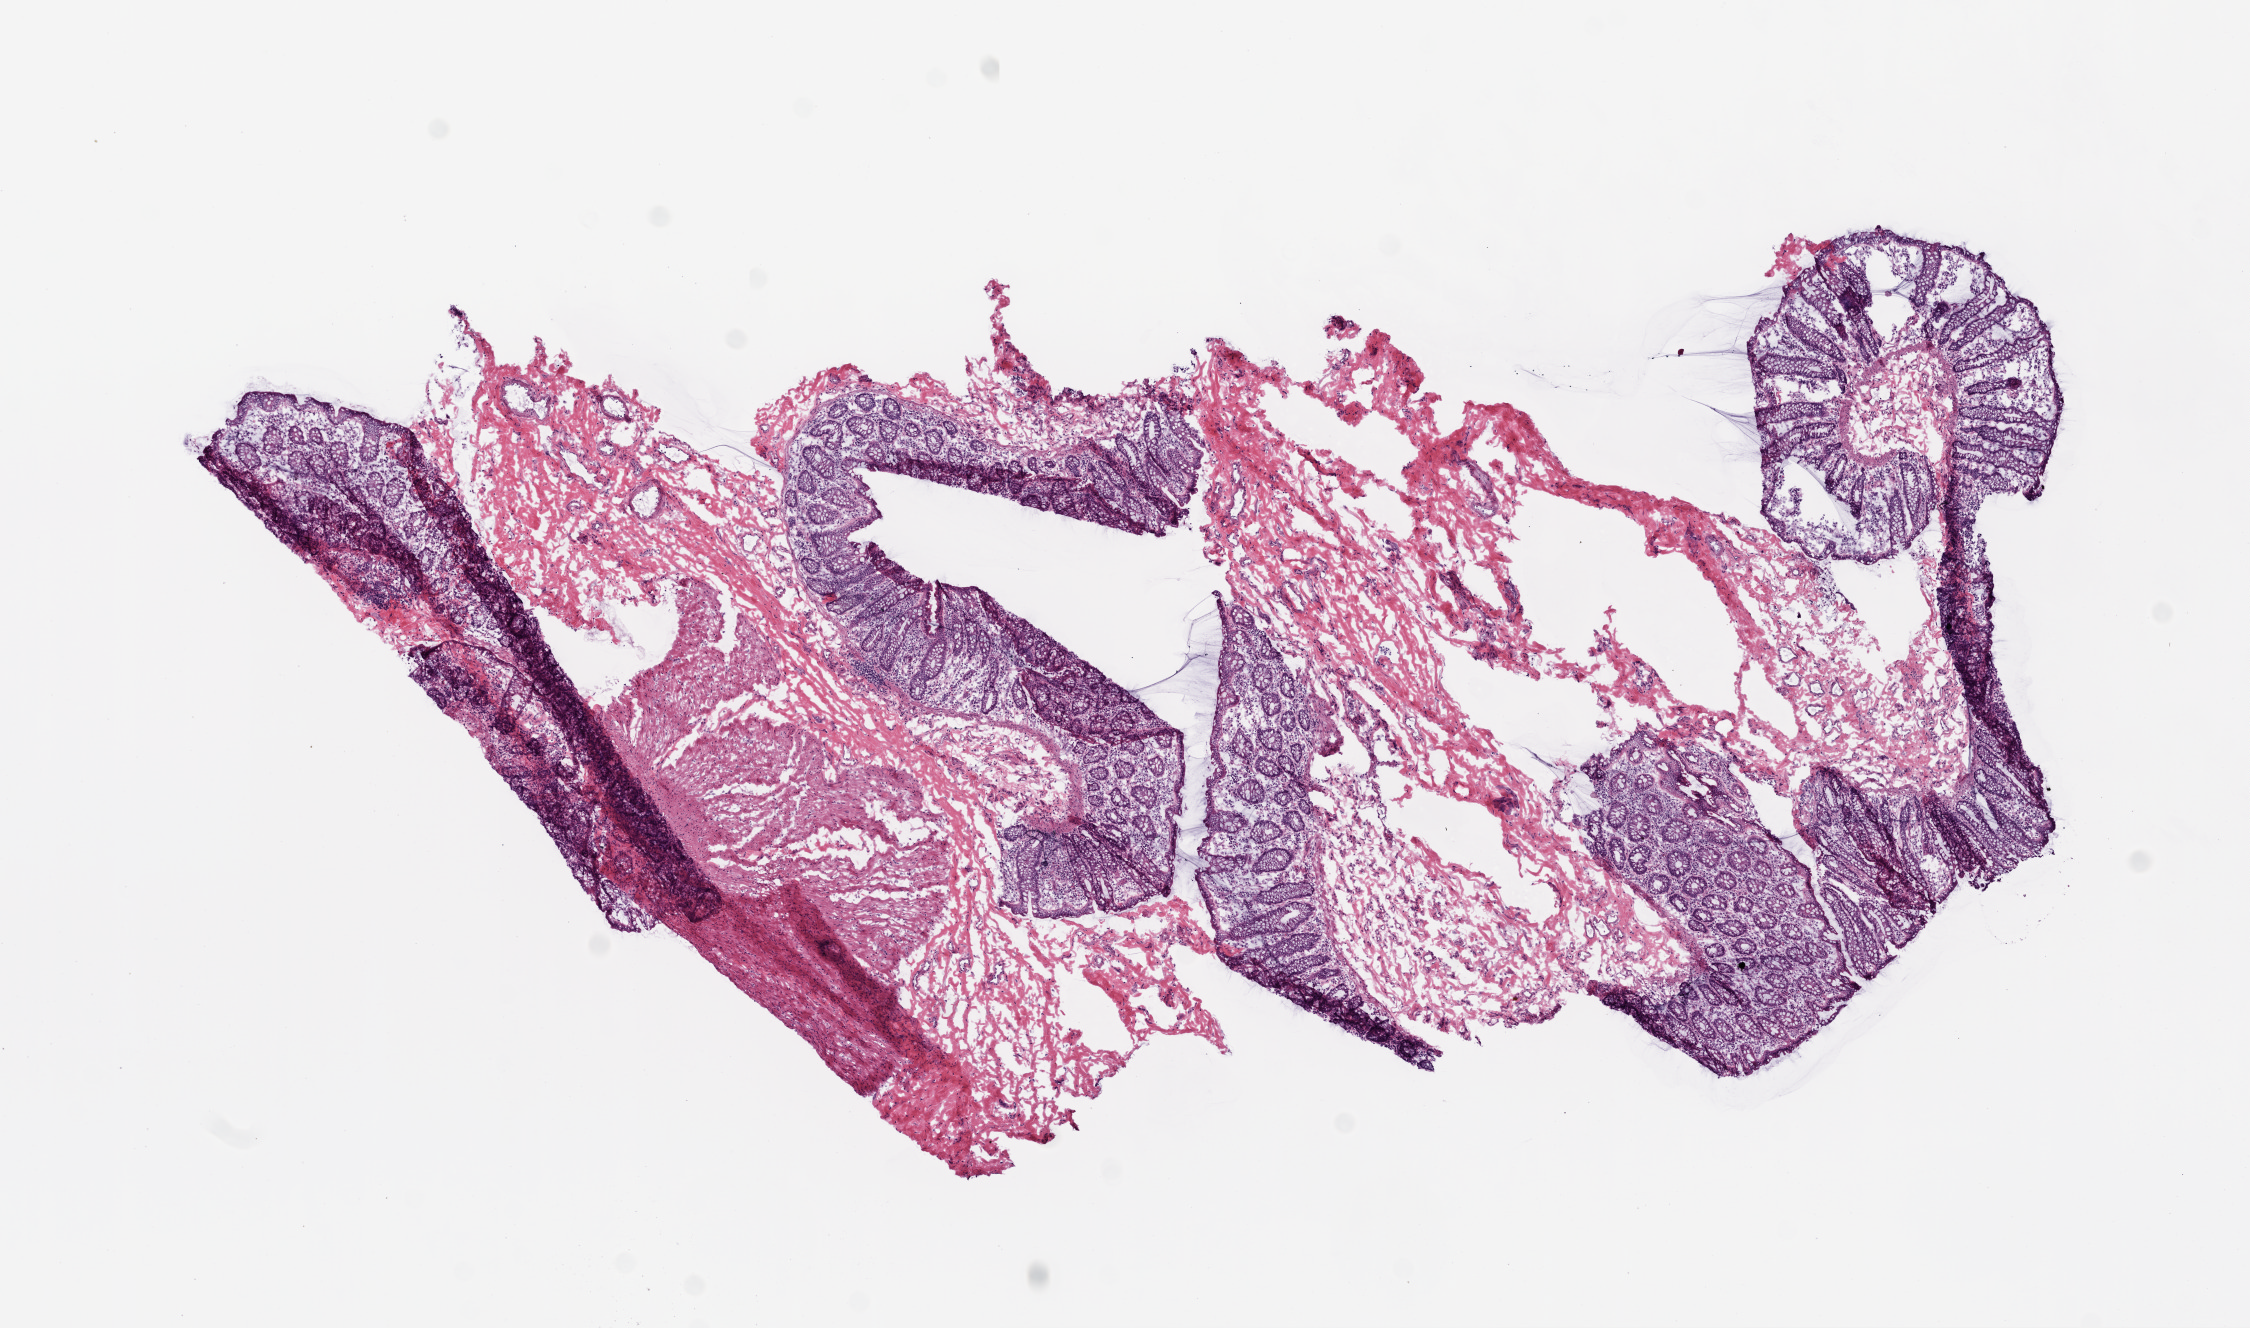
Whole-slide histology image, Hematoxylin and eosin (H&E) stained — a low-resolution overview of the entire scanned area, about 9.0 x 5.3 mm (acquisition: 20x scan), frozen section, colon, solid tissue normal (non-tumour tissue) sample. Patient: female, age at initial diagnosis 74 years.
This section: solid tissue normal sample (biorepository sample class). Patient diagnosis: Mucinous adenocarcinoma.